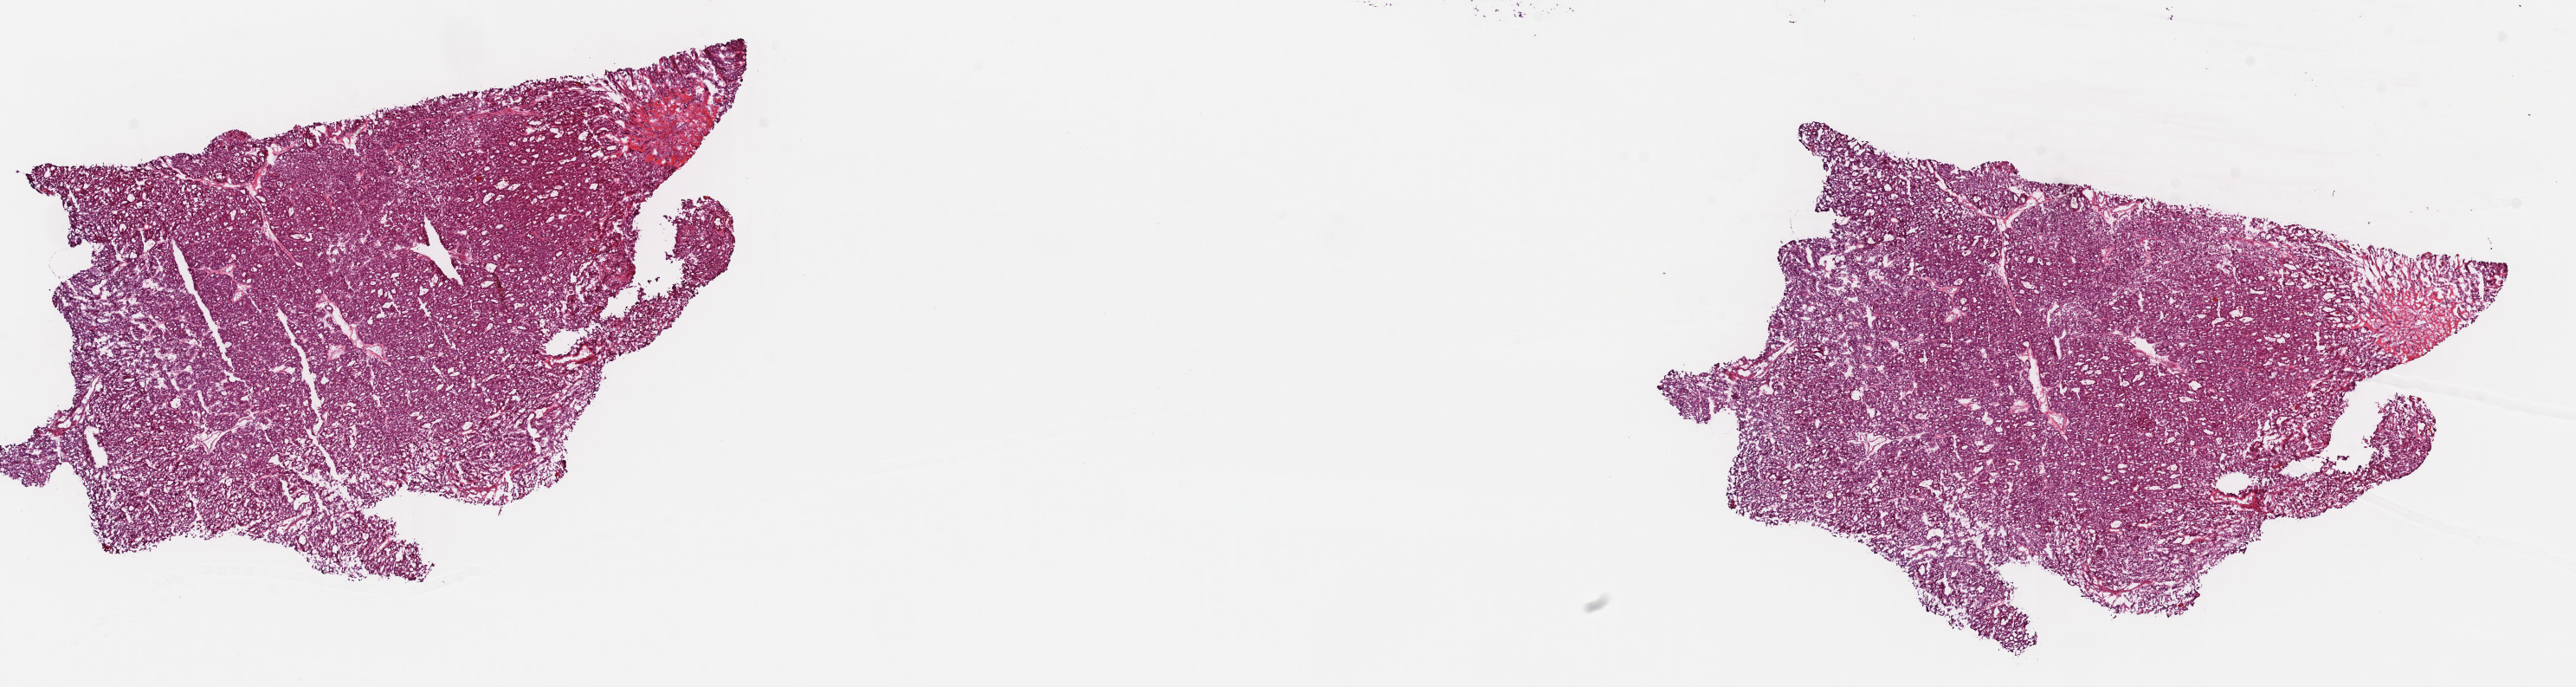
Digitized H&E tissue section (whole slide), whole scanned area (about 23.5 x 6.3 mm, slide scanned at 40x) shown as a low-resolution overview. Frozen section. Thyroid, primary tumour sample. Female patient; age at initial diagnosis 46 years. Composition of this section per pathologist review: tumour cells 85%, tumour nuclei 85%, normal cells 0%, stromal cells 15%, necrosis 0%. Infiltration values recorded for this section: lymphocyte infiltration 0%, monocyte infiltration 0%, neutrophil infiltration 0%.
TNM: T2 N0 MX. AJCC pathologic stage: II. Pathologic diagnosis: Papillary carcinoma, follicular variant. Lymph nodes positive (case pathology): 0 of 1 examined.